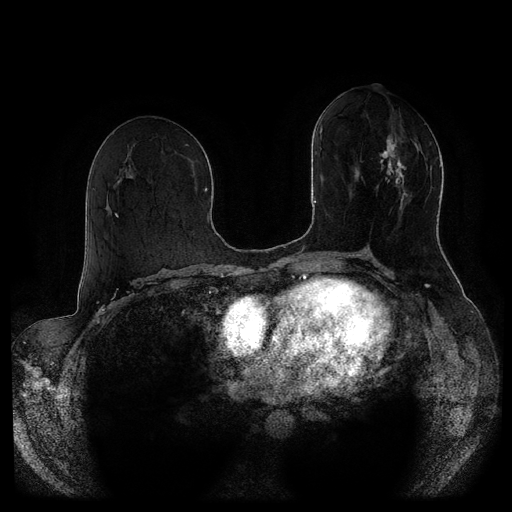
Breast MRI (dynamic contrast-enhanced, multi-phase), one axial slice; position 47 of 116 along the scan axis; dynamic contrast-enhanced series, time point 2 of 5 at this slice position (early post-contrast); 1.5 T; TE 2.6 ms, TR 5.3 ms; 2 mm slice thickness; 512 × 512 image matrix, field of view 370 × 370 mm. Female patient, age 51 years.
Structures marked on this image (semi-automatic segmentation, software-assisted and operator-edited):
- breast lesion (labelled 'tumour' in the annotation; benign lesions carry a separate 'benign' label): box from (x=376, y=132) to (x=408, y=213) px